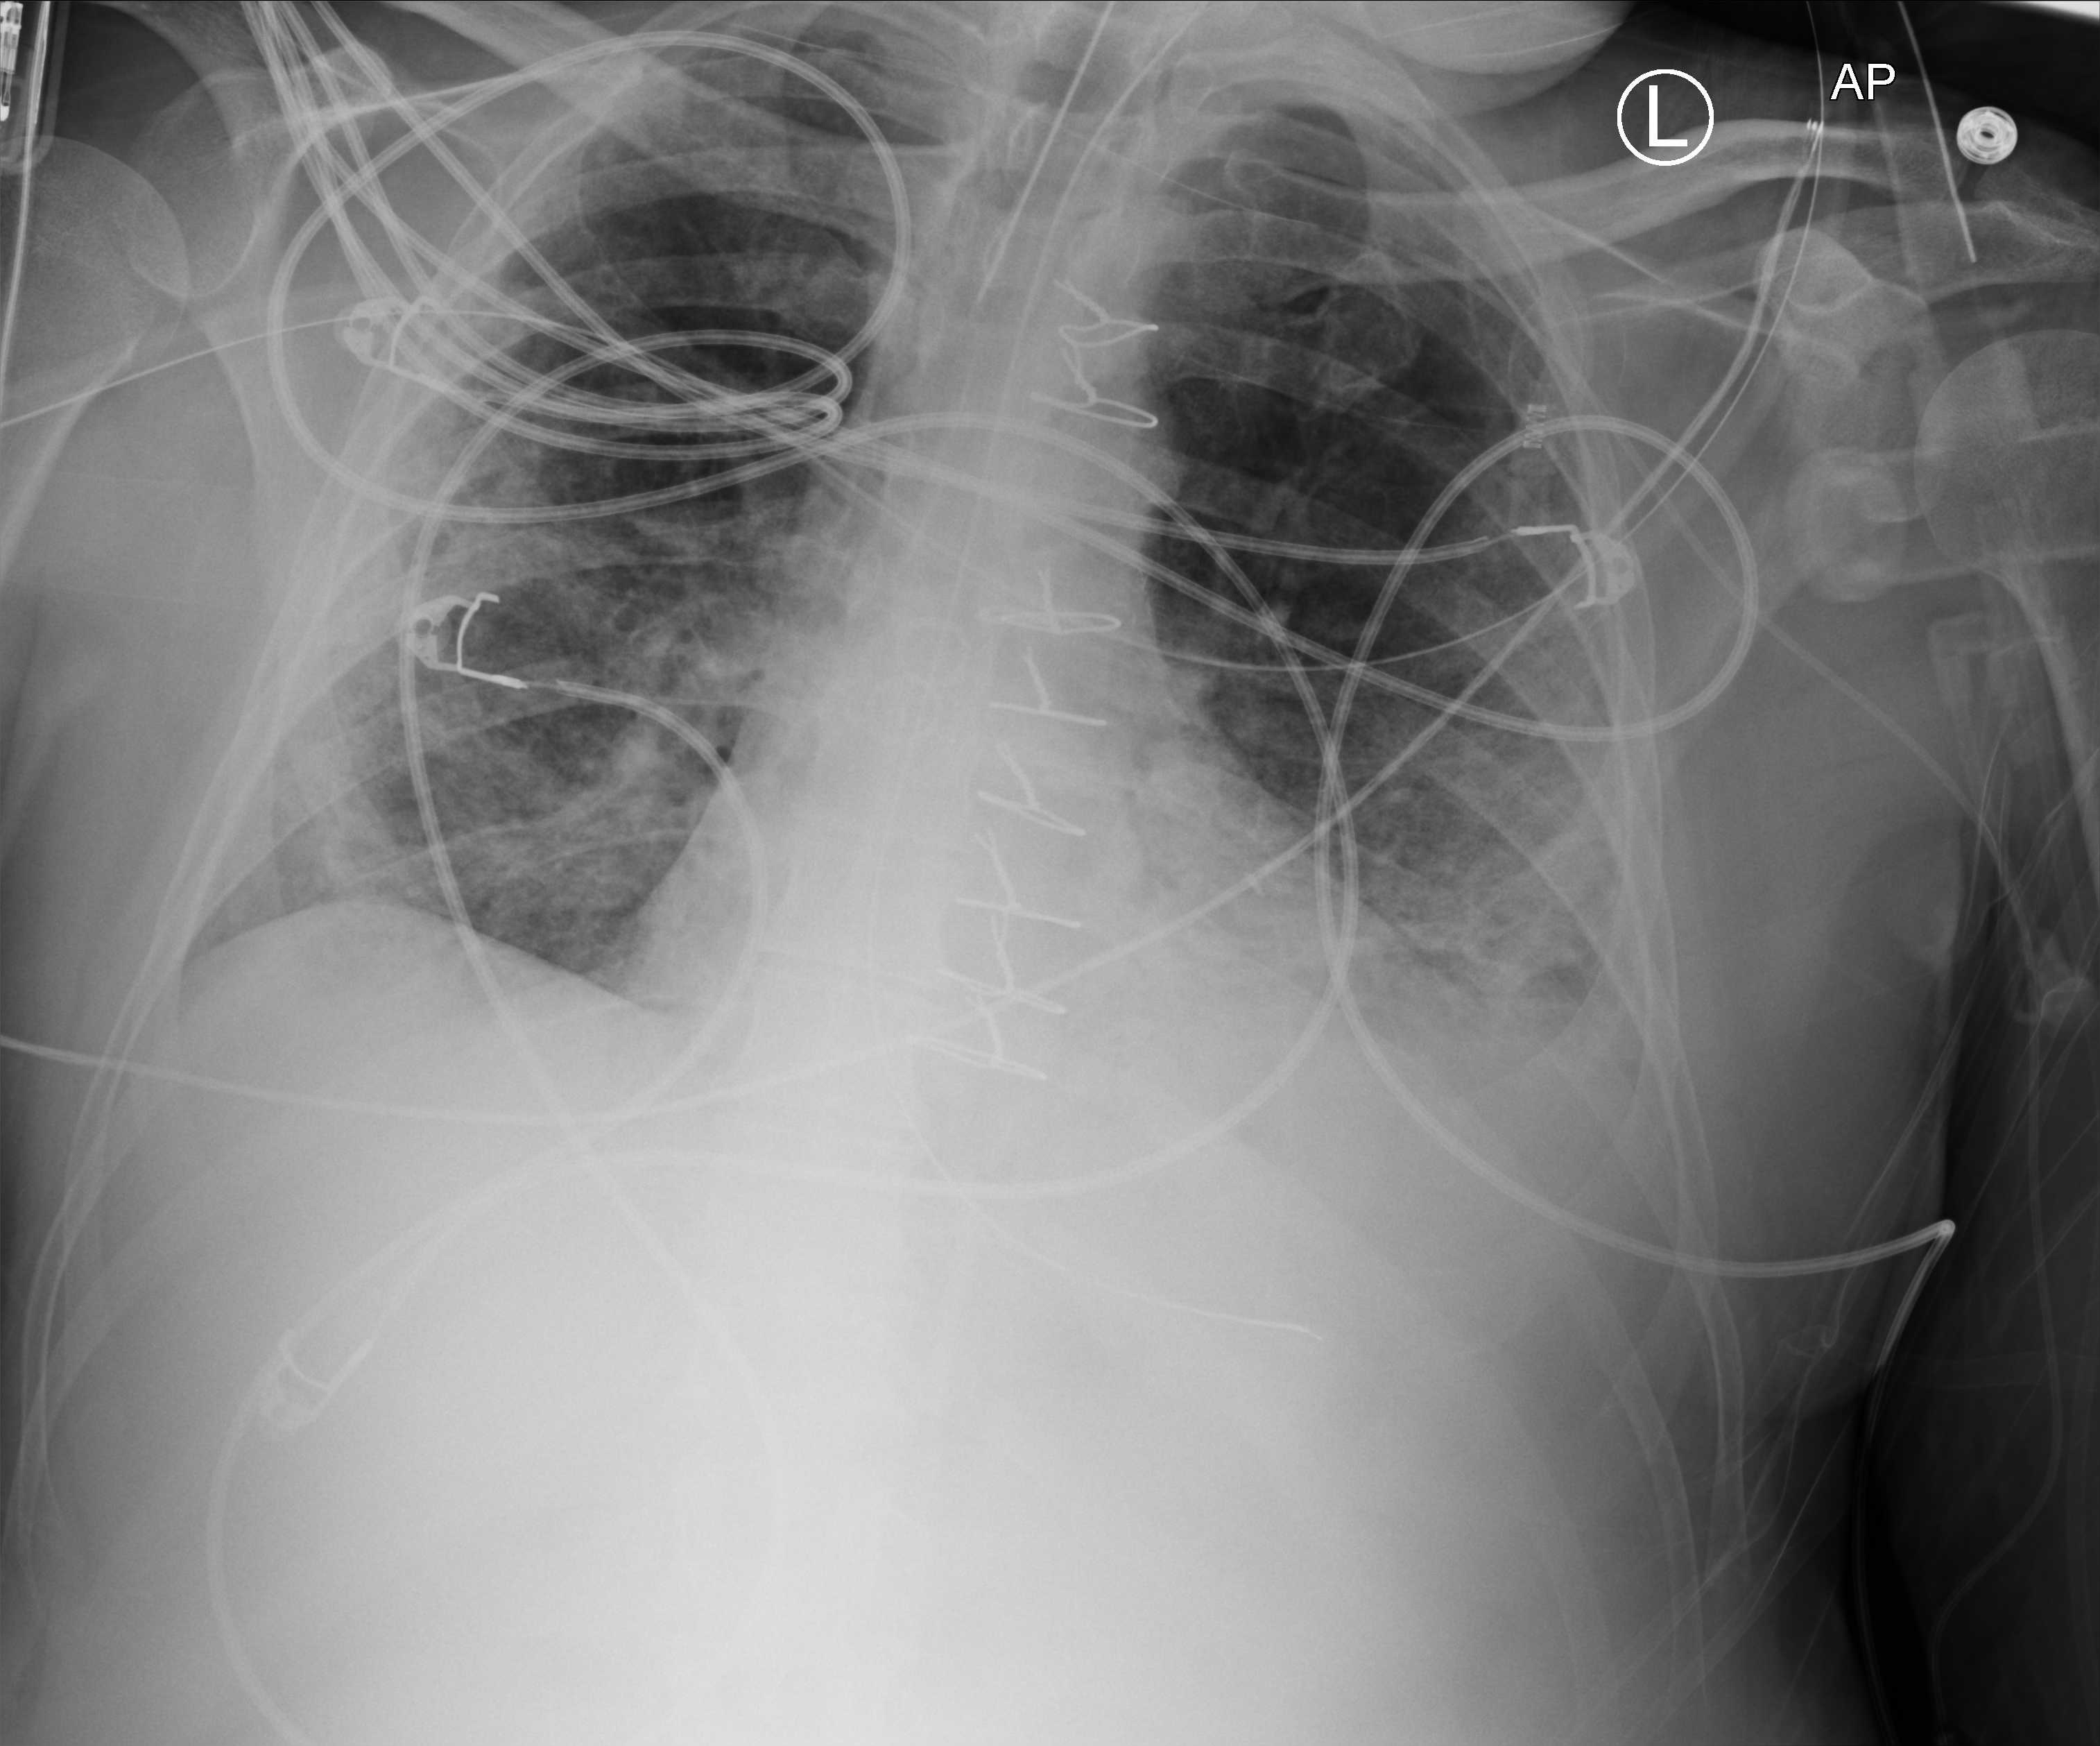
Portable chest radiograph; anteroposterior (AP) projection. Male patient hospitalised with COVID-19, age 18–59 years.
Admission-level facts for this patient (not findings on this image; timing relative to this image not recorded):
- mechanically ventilated during this hospital stay: yes
- admitted to intensive care during this hospital stay: yes